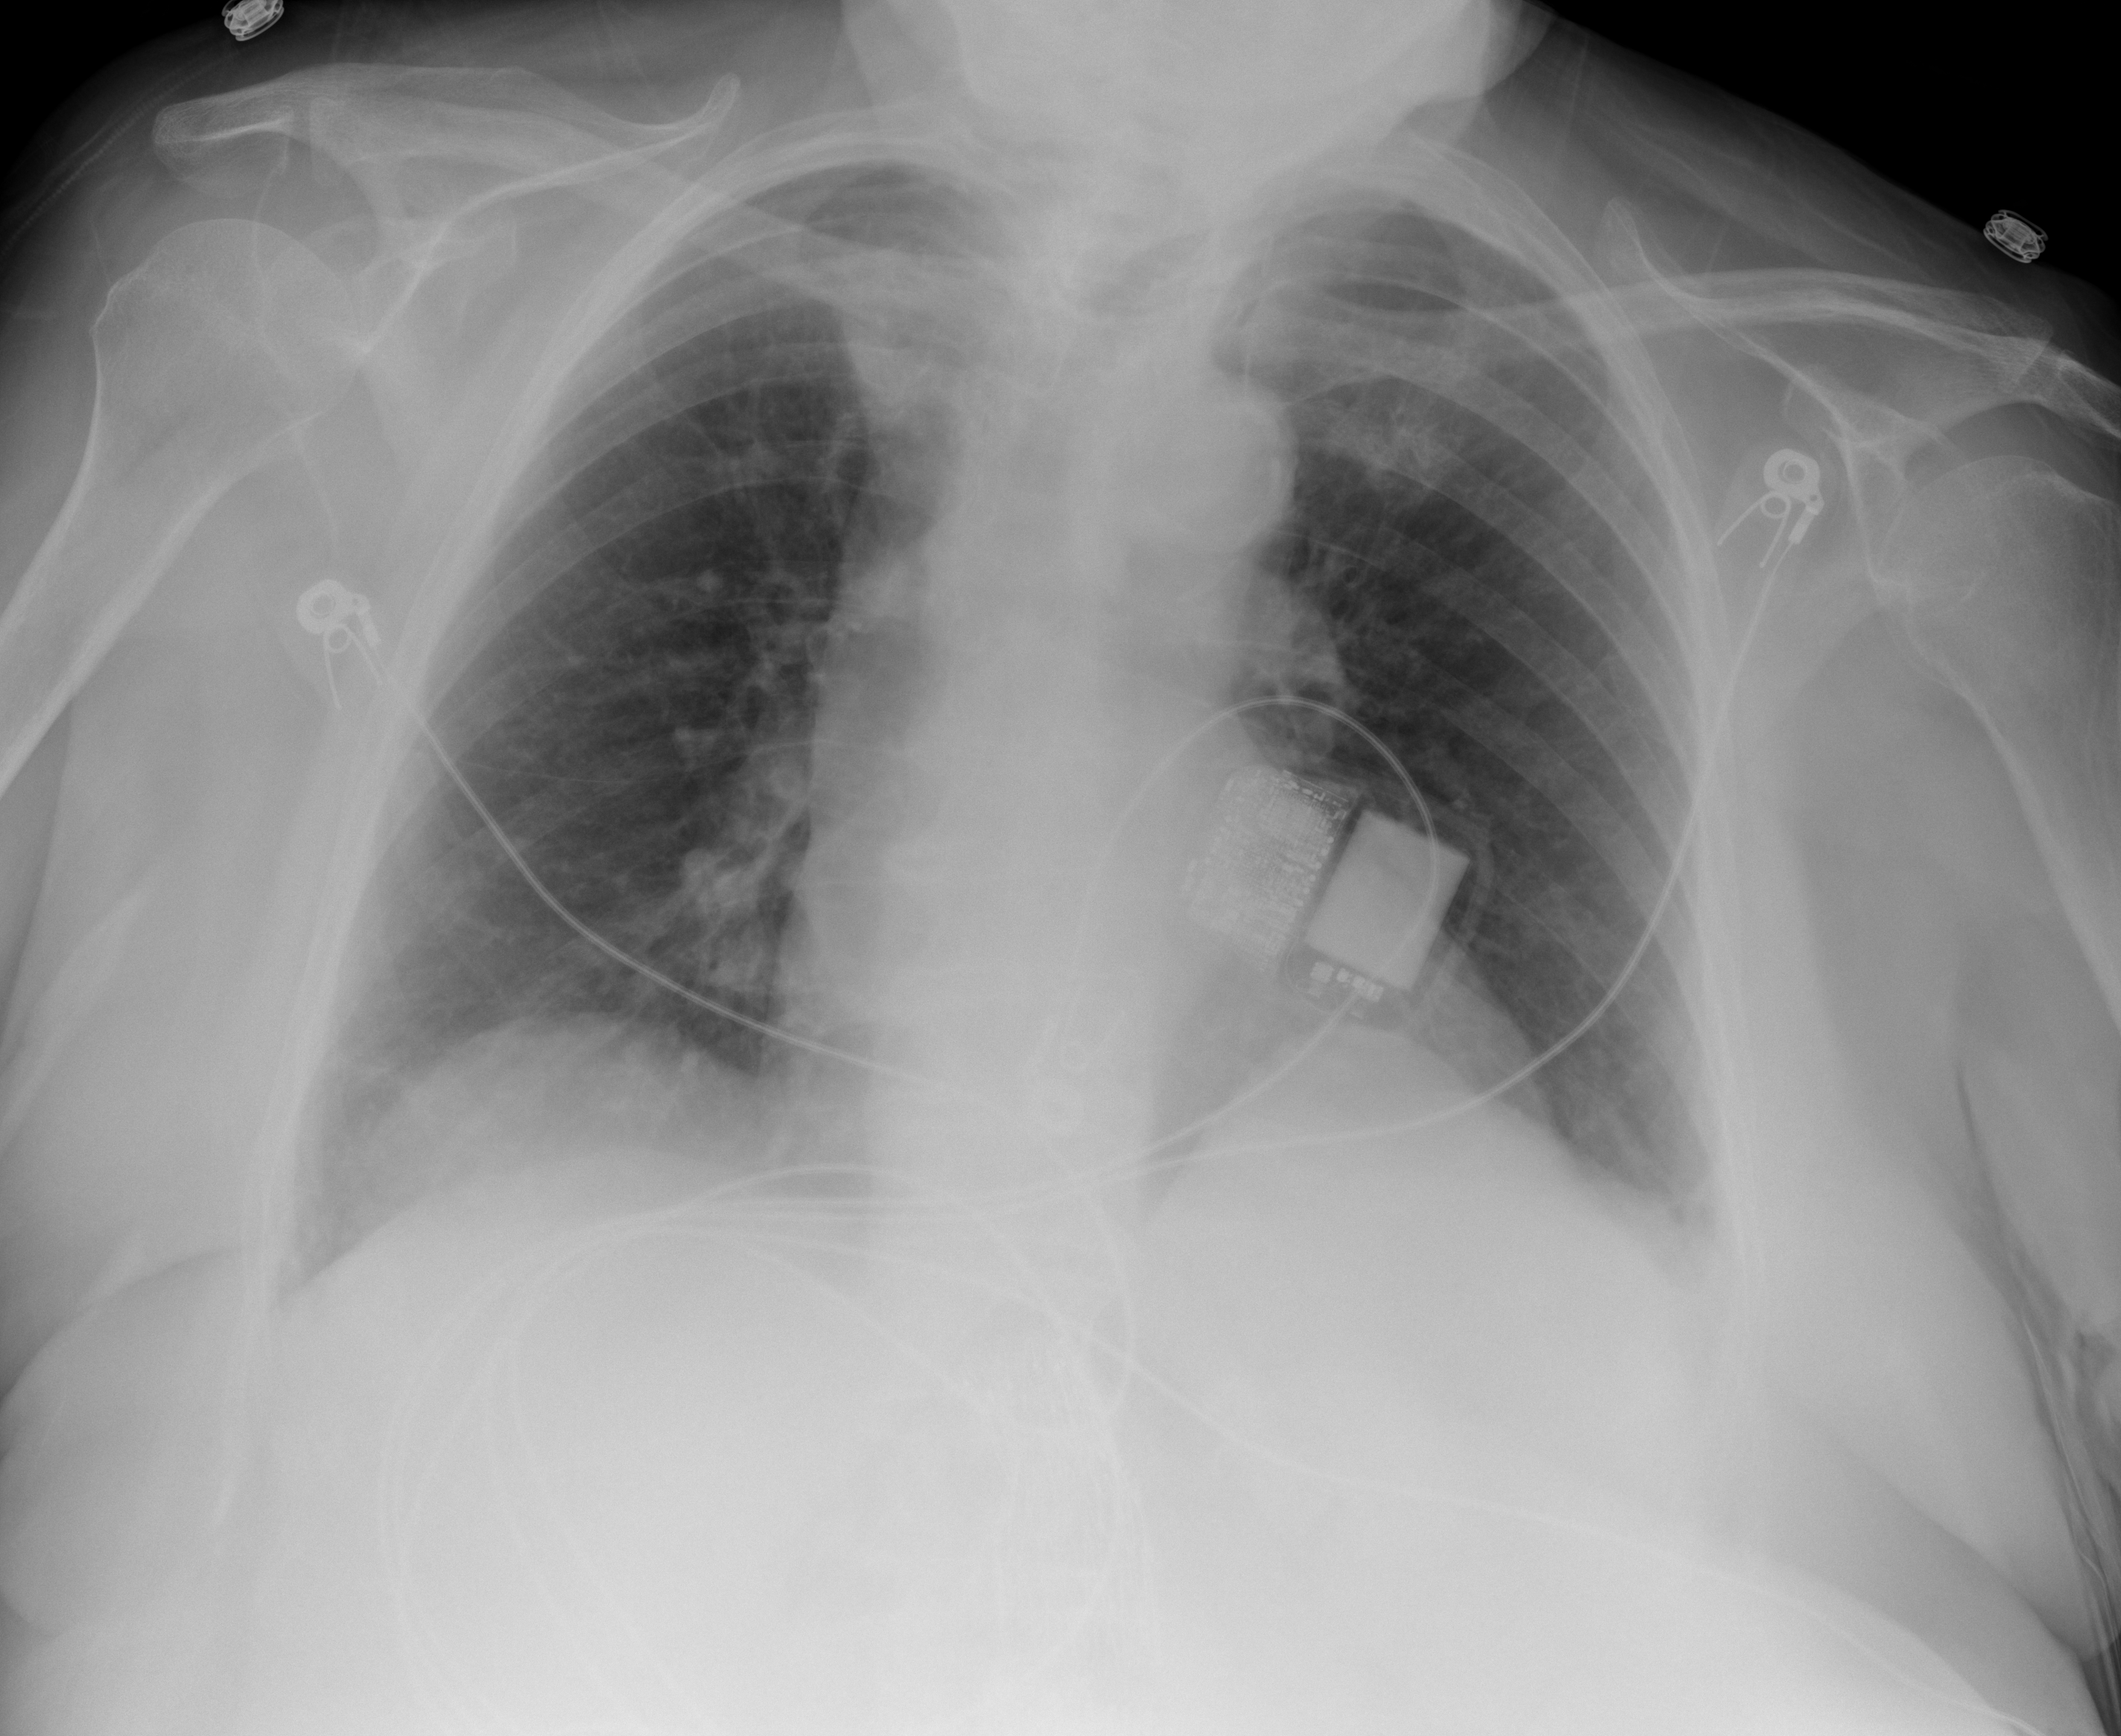
Chest X-ray (portable), AP projection. Female patient, age 88 years; COVID-19 (test-positive).
Radiologist's key findings for this exam: The lungs are clear and without focal consolidation.